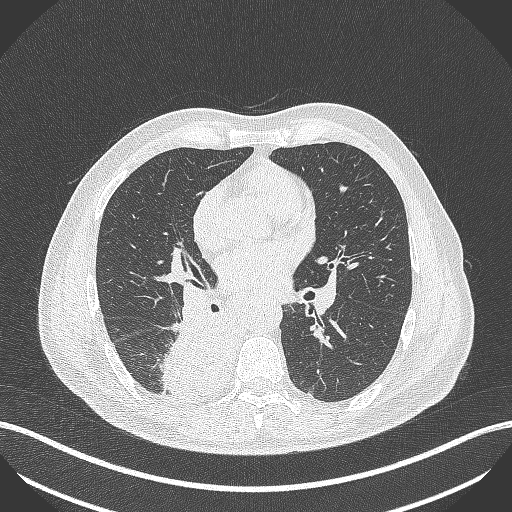
Chest CT, one axial slice; position 242 of 451 along the scan axis; reconstruction kernel B70f; lung window (W 1500 / L -600 HU); 1 mm slice thickness; 512 × 512 image matrix, field of view 400 × 400 mm. Patient: male, 61 years. From the clinical record (not read from this slice): clinical TNM (as recorded): T1 N0 M0; histopathological grade: G3.
Annotated regions visible in this slice (rectangle marked by the reading radiologist):
- lung tumour (recorded histology: small cell carcinoma): bounding box [x1, y1, x2, y2] px = [160, 316, 241, 397]